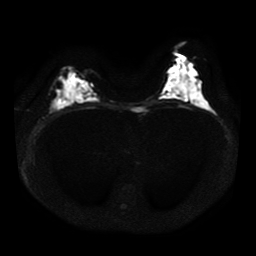
Breast MRI, one axial slice. Position 23 of 41 along the scan axis. Diffusion-weighted series; image 2 of 4 stored at this slice position (different b-values; order by instance number). 1.5 T. 5 mm slice thickness. 256 × 256 image matrix, field of view 330 × 330 mm. Female patient.
Annotated regions visible in this slice (manually delineated by an expert):
- tumour on diffusion-weighted imaging: box from (x=64, y=101) to (x=71, y=107) px